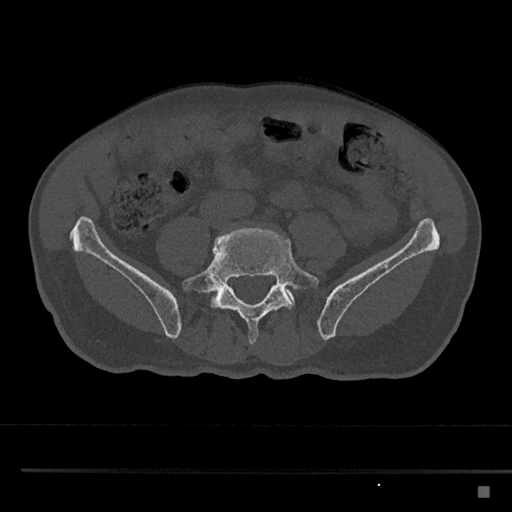
CT including the spine, one axial slice; slice 582 of 797 in the series (ordered by position); bone window (W 1800 / L 400 HU); 0.5 mm slice thickness; 512 × 512 image matrix, field of view 391 × 391 mm. Male patient, age 59 years. From the clinical record (not read from this slice): primary cancer: prostate.
Structures marked on this image (semi-automatic segmentation, software-assisted and operator-edited):
- L5 vertebra: bounding box [x1, y1, x2, y2] px = [182, 228, 319, 345]